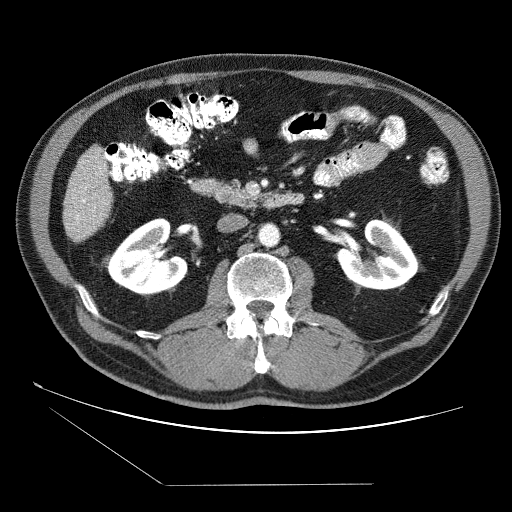
Contrast-enhanced abdominal CT (liver protocol), one axial slice; position 12 of 87 along the scan axis; reconstruction kernel STANDARD; 120 kVp; soft-tissue window (W 400 / L 40 HU); 512 × 512 image matrix, field of view 400 × 400 mm. From the clinical record (not read from this slice): diagnosis: hepatocellular carcinoma (patient treated with transarterial chemoembolisation; whether this scan precedes or follows treatment is not stated here); TNM stage (as recorded): Stage-II; Child-Pugh class: B; tumour differentiation: no biopsy; tumour nodularity: multinodular.
Structures marked on this image (semi-automatically segmented with operator editing):
- liver parenchyma outside the tumour (the mass and vessels are separate outlines, so this box may not span the whole liver): box from (x=64, y=146) to (x=112, y=241) px
- liver vessels: (x=70, y=157)–(x=103, y=223)